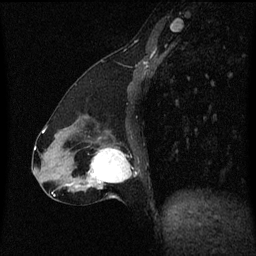
Breast MRI (dynamic contrast-enhanced), one sagittal slice; slice 23 of 60 in the series (ordered by position); dynamic contrast-enhanced series, image 2 of 3 at this slice position (ordered by acquisition); 1.5 T; TE 4.2 ms, TR 8.4 ms; 256 × 256 image matrix, field of view 200 × 200 mm. Patient: female, 47 years.
Structures marked on this image (semi-automatic segmentation, software-assisted and operator-edited):
- analysis volume of interest (the breast-tissue region the enhancement analysis was run in; not a lesion): bounding box (x1, y1, x2, y2) in pixels: (81, 142, 137, 197)
- tumour enhancement mask (voxels above the 70 % enhancement threshold inside the analysis volume of interest): (90, 148, 131, 185)